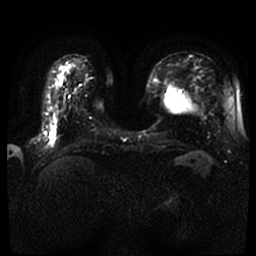
Breast MRI, one axial slice; slice 13 of 59 in the series (ordered by position); diffusion-weighted series; image 2 of 4 stored at this slice position (different b-values; order by instance number); 1.5 T; 256 × 256 image matrix. Female patient.
Outlined on this slice (manually delineated by an expert):
- tumour on diffusion-weighted imaging: bounding box <50,125,58,139> (left, top, right, bottom; pixels)